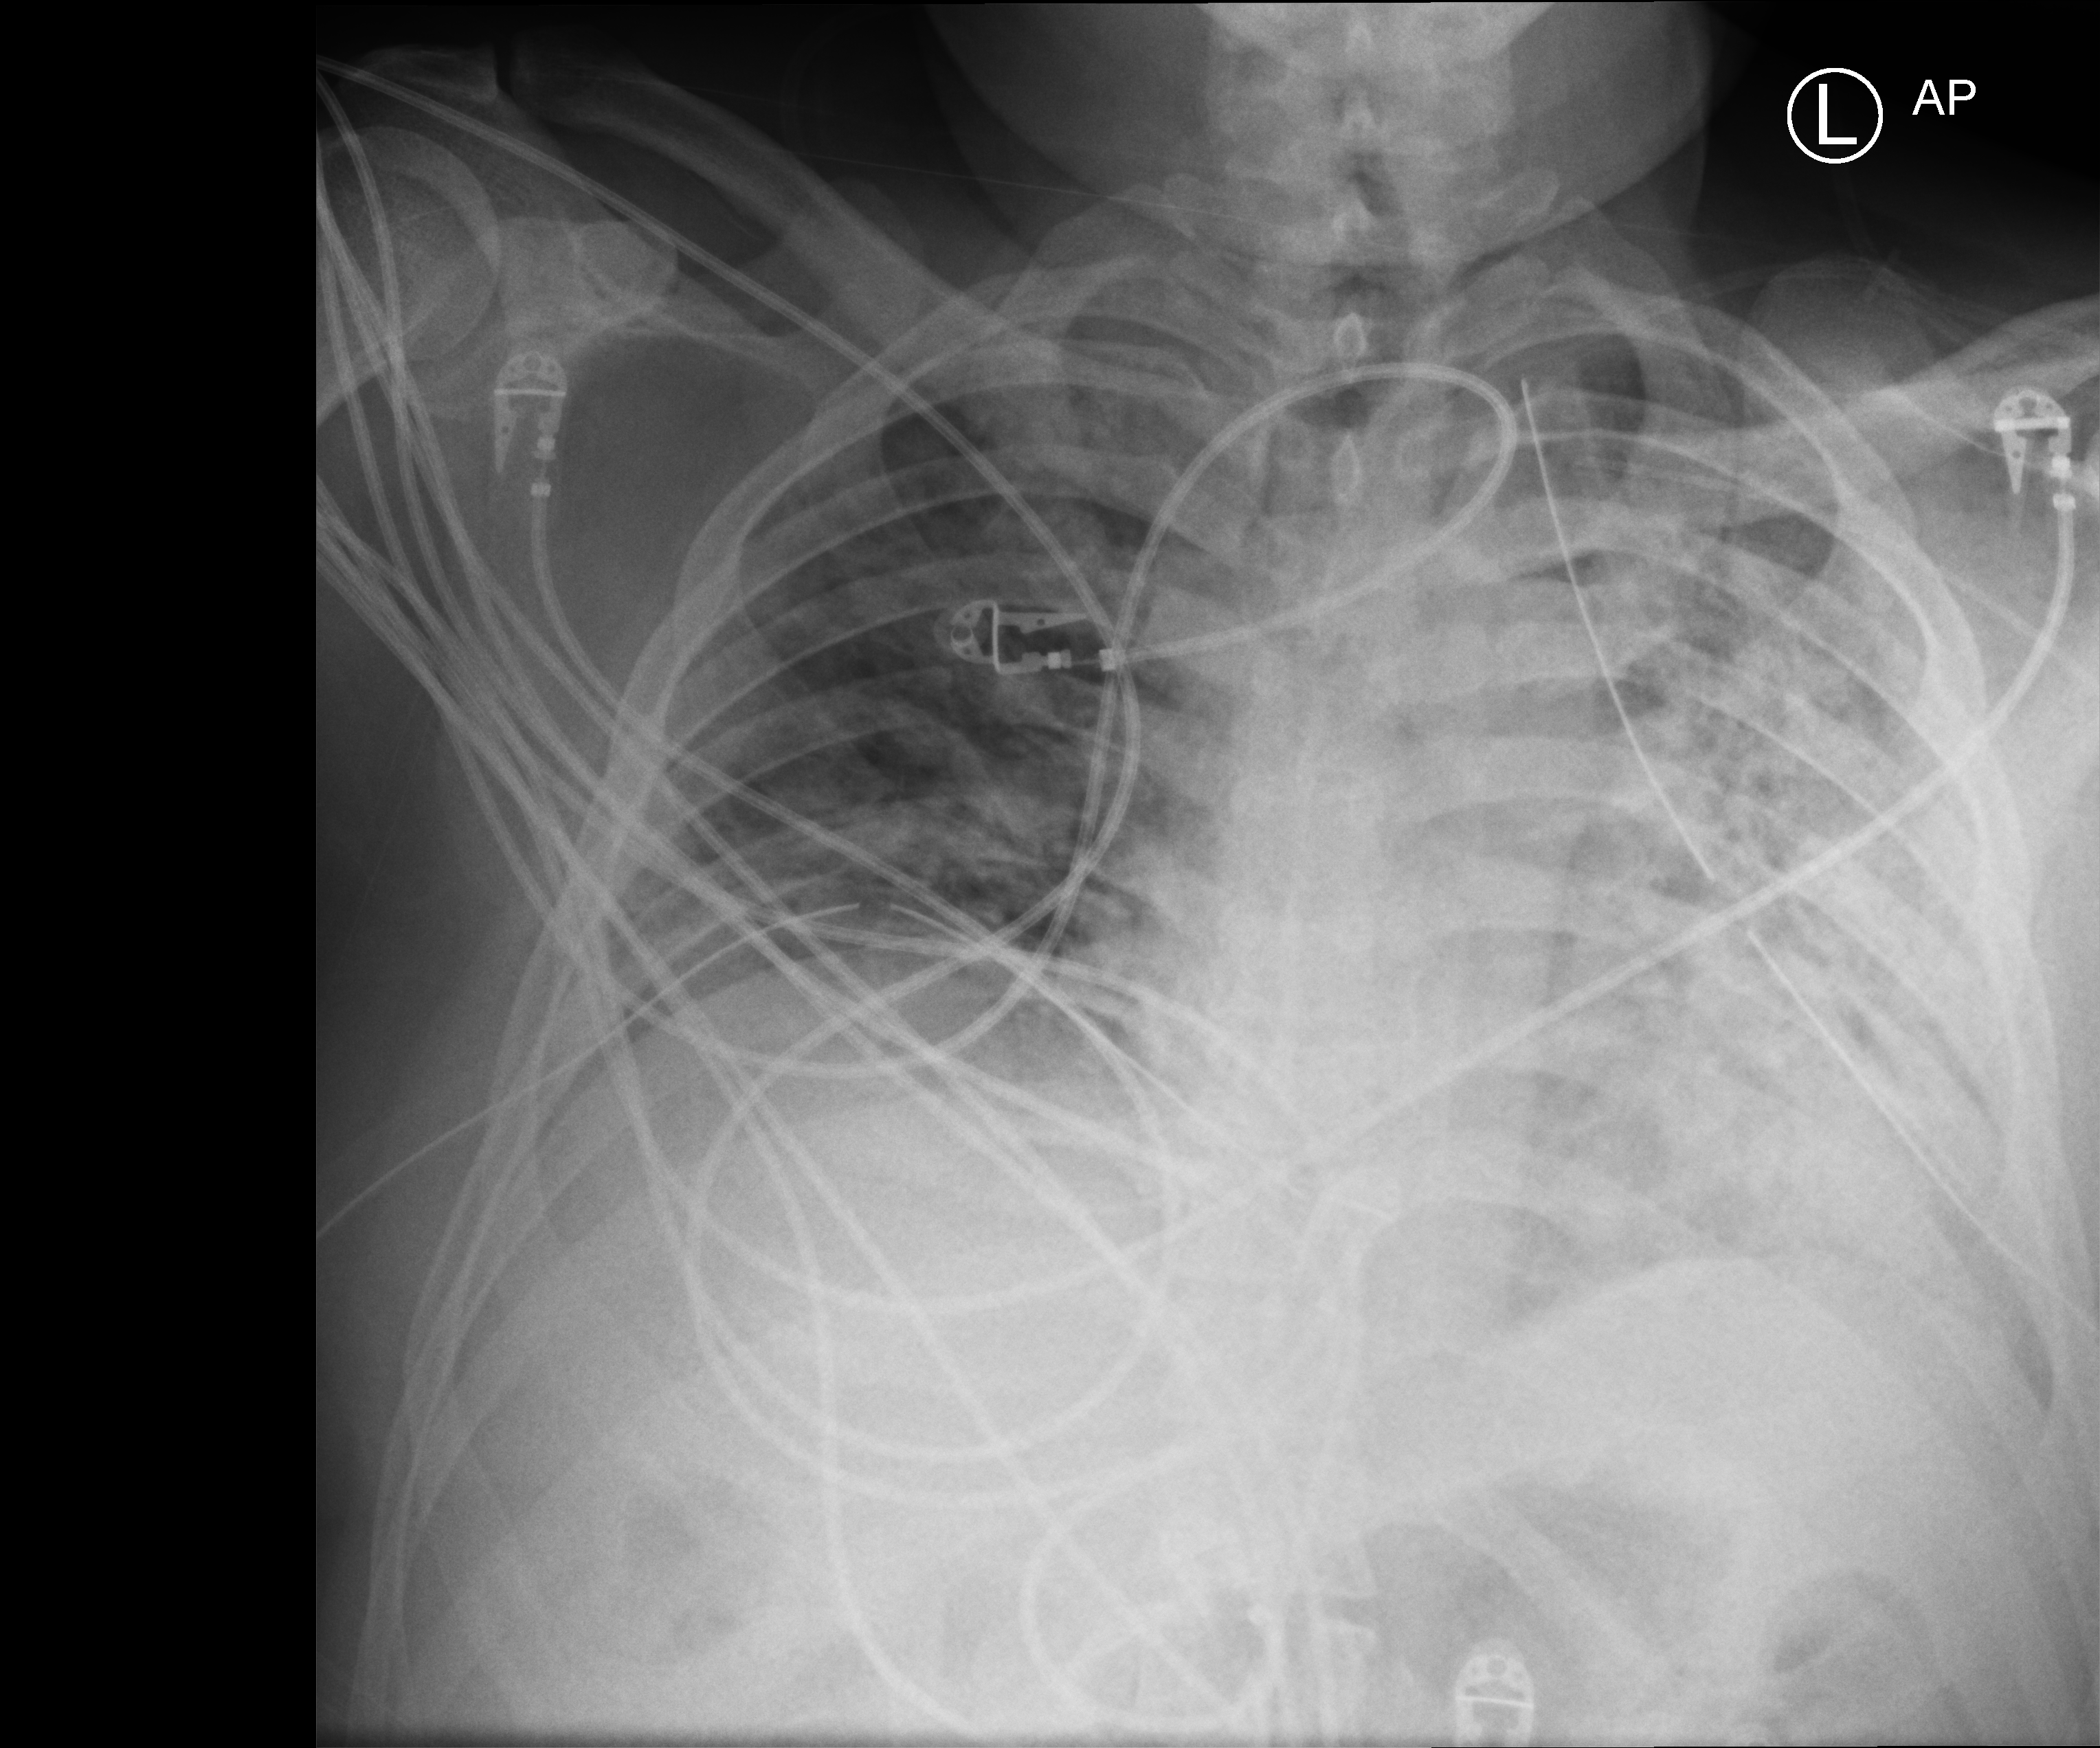
Bedside chest radiograph (computed radiography). Patient hospitalised with COVID-19; male, aged 18–59 years.
Admission-level facts for this patient (not findings on this image; timing relative to this image not recorded): admitted to intensive care during this hospital stay: yes; mechanically ventilated during this hospital stay: yes.